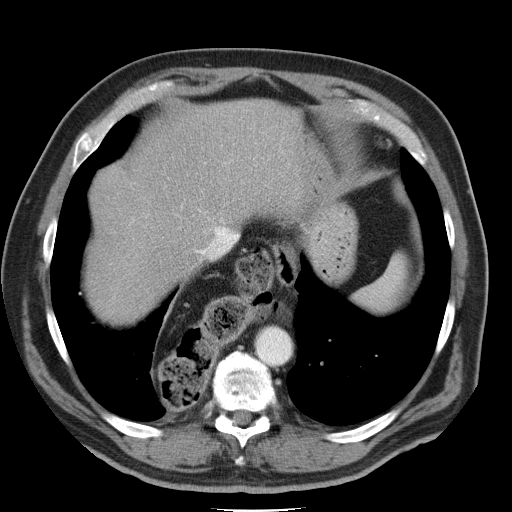
Contrast-enhanced abdominal CT, one axial slice. Slice 39 of 45 in the series (ordered by position). Intravenous contrast given. Soft-tissue window (W 400 / L 40 HU). 5 mm slice thickness. 512 × 512 image matrix, field of view 386 × 386 mm. Male patient, age 65 years. From the clinical record (not read from this slice): diagnosis: colorectal cancer liver metastases, imaged before liver resection; multiple liver metastases: yes; largest metastasis: 4.9 cm; disease in both lobes: no.
Outlined on this slice (outlined manually by an expert reader):
- hepatic veins: bounding box (x1, y1, x2, y2) in pixels: (113, 218, 235, 300)
- liver: (87, 100, 295, 317)
- planned liver remnant (the part of the liver to remain after resection): (123, 100, 295, 243)
- portal vein (with intrahepatic branches): (127, 215, 138, 228)